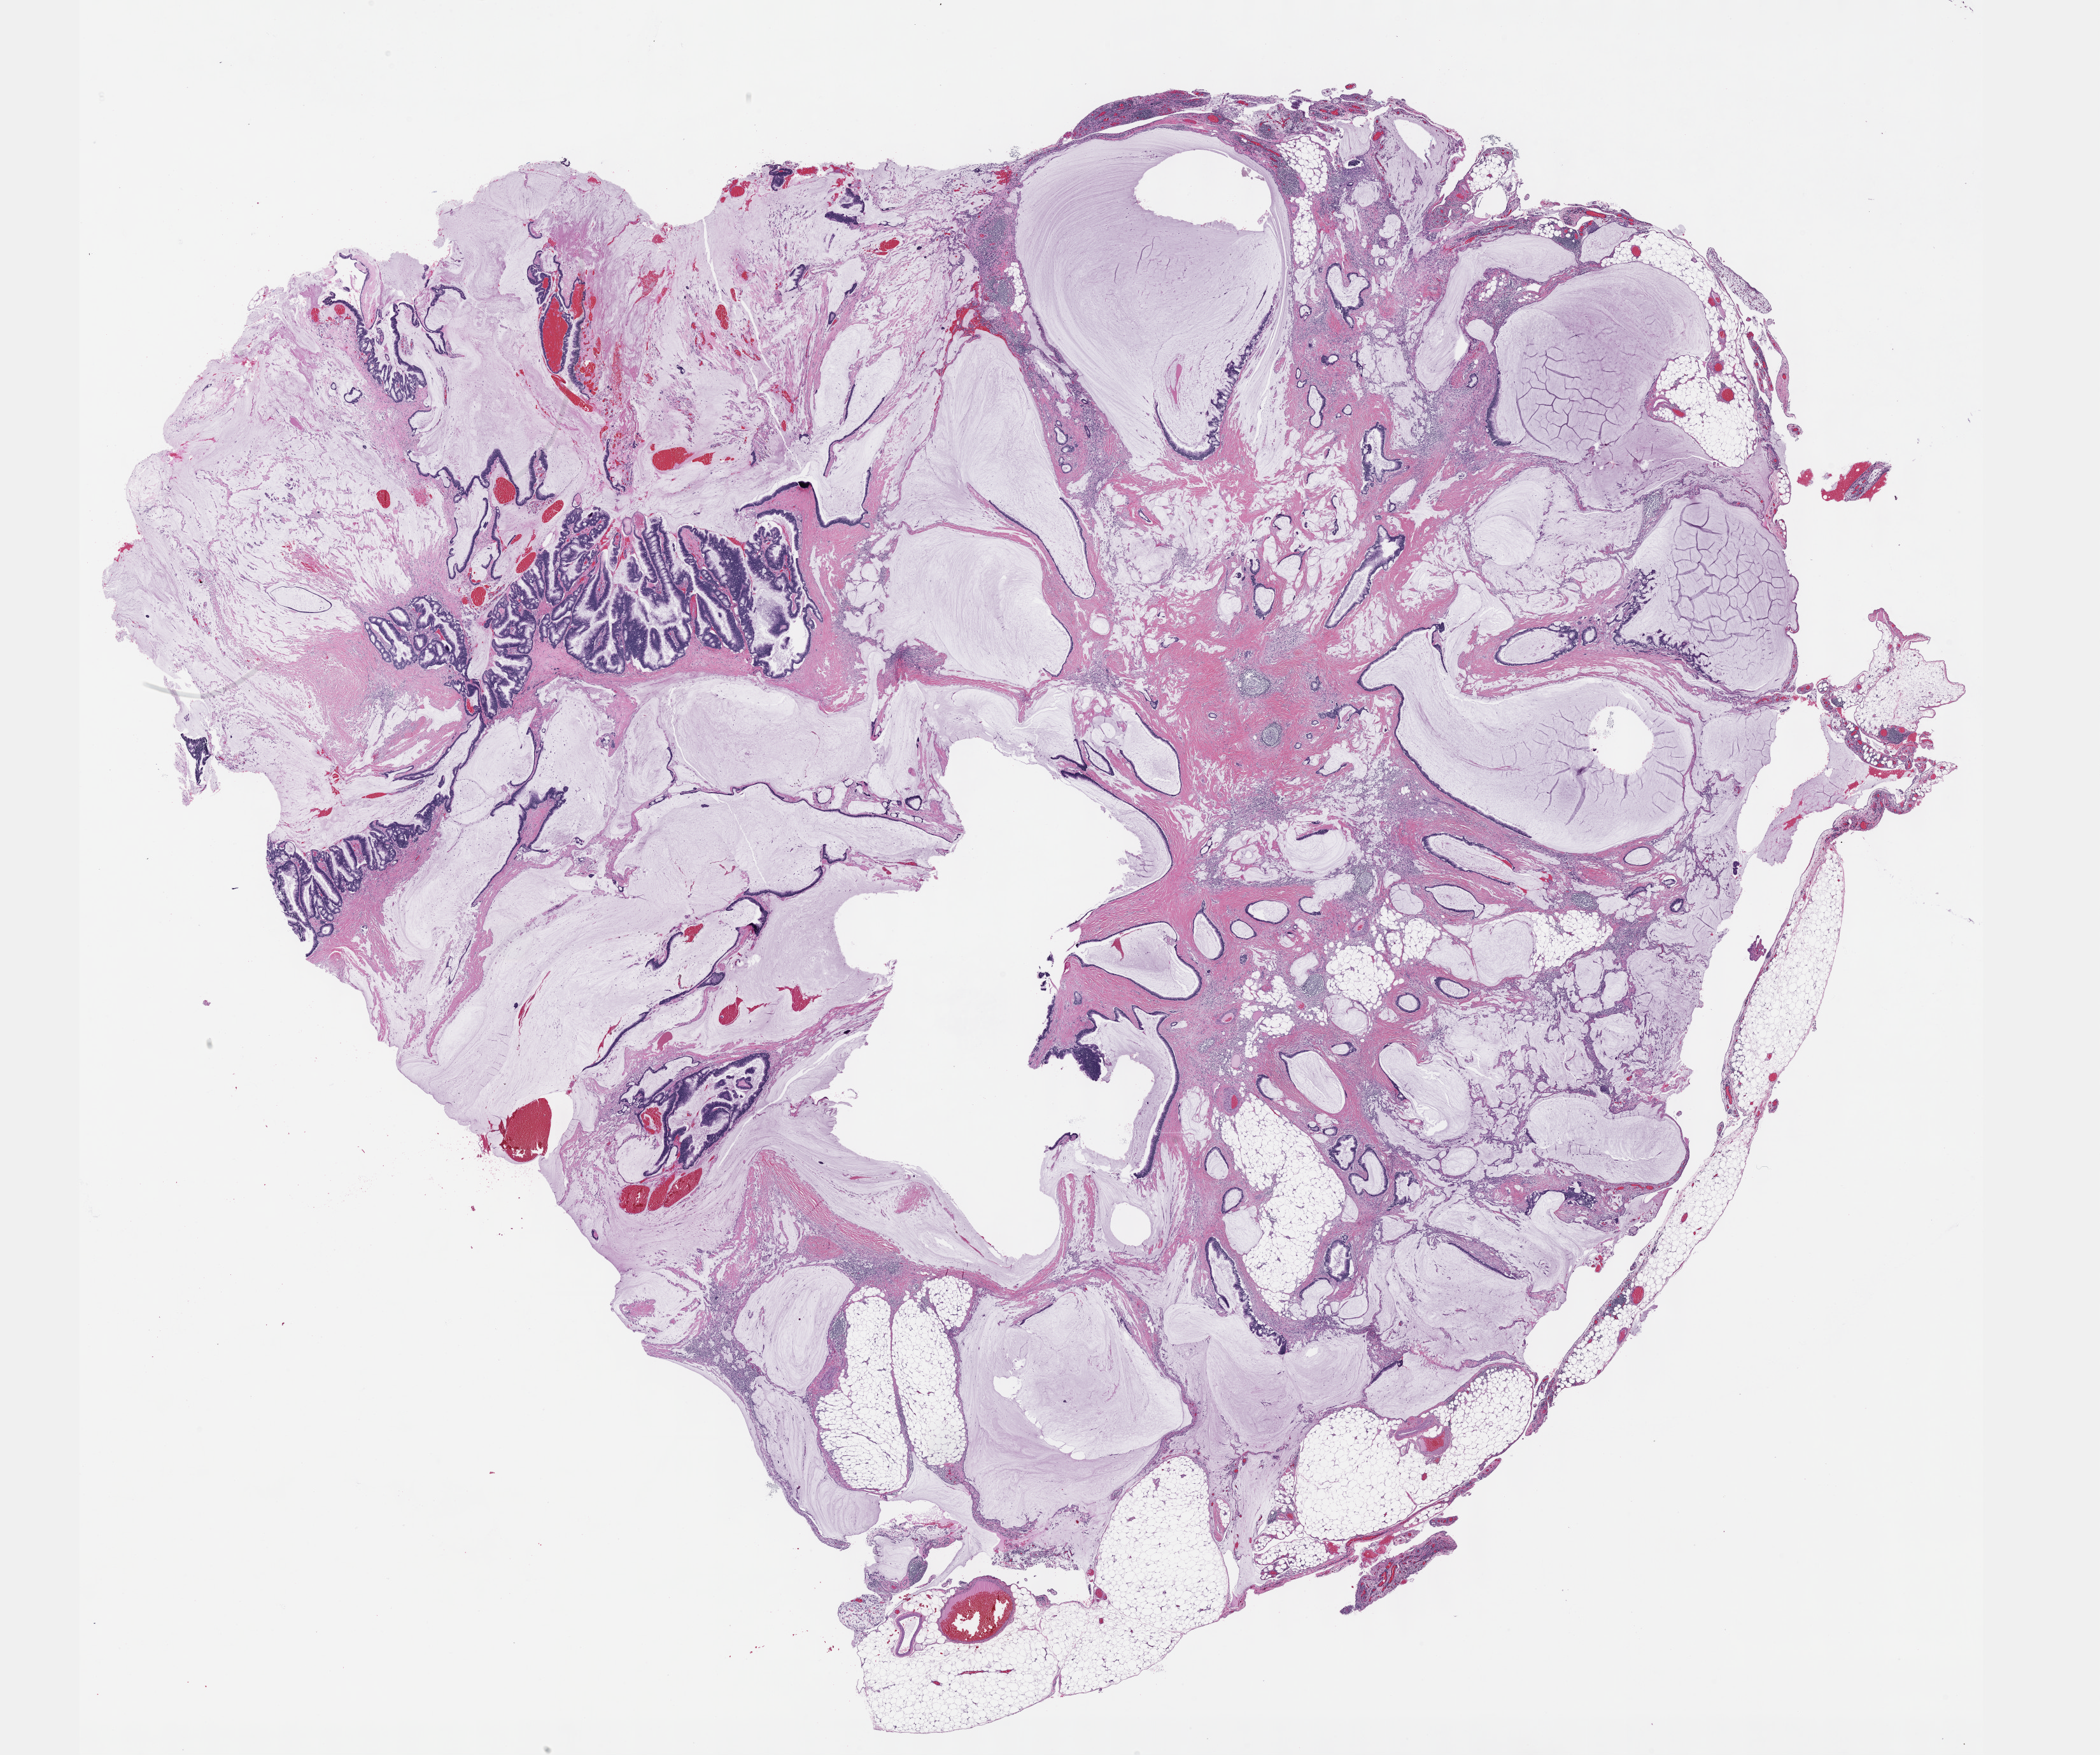
Hematoxylin and eosin (H&E) stained whole-slide image — low-resolution overview of the scanned area, about 26.7 x 22.3 mm (slide scanned at 40x). Formalin-fixed paraffin-embedded (FFPE) diagnostic section. Primary tumour sample from the colon. Female, age 66 years at initial diagnosis.
Pathologic diagnosis: Mucinous adenocarcinoma (descending colon). AJCC pathologic stage: IVB (7th edition). TNM: T4b N1b M1b. Lymph nodes positive (case pathology): 3 of 19 examined.